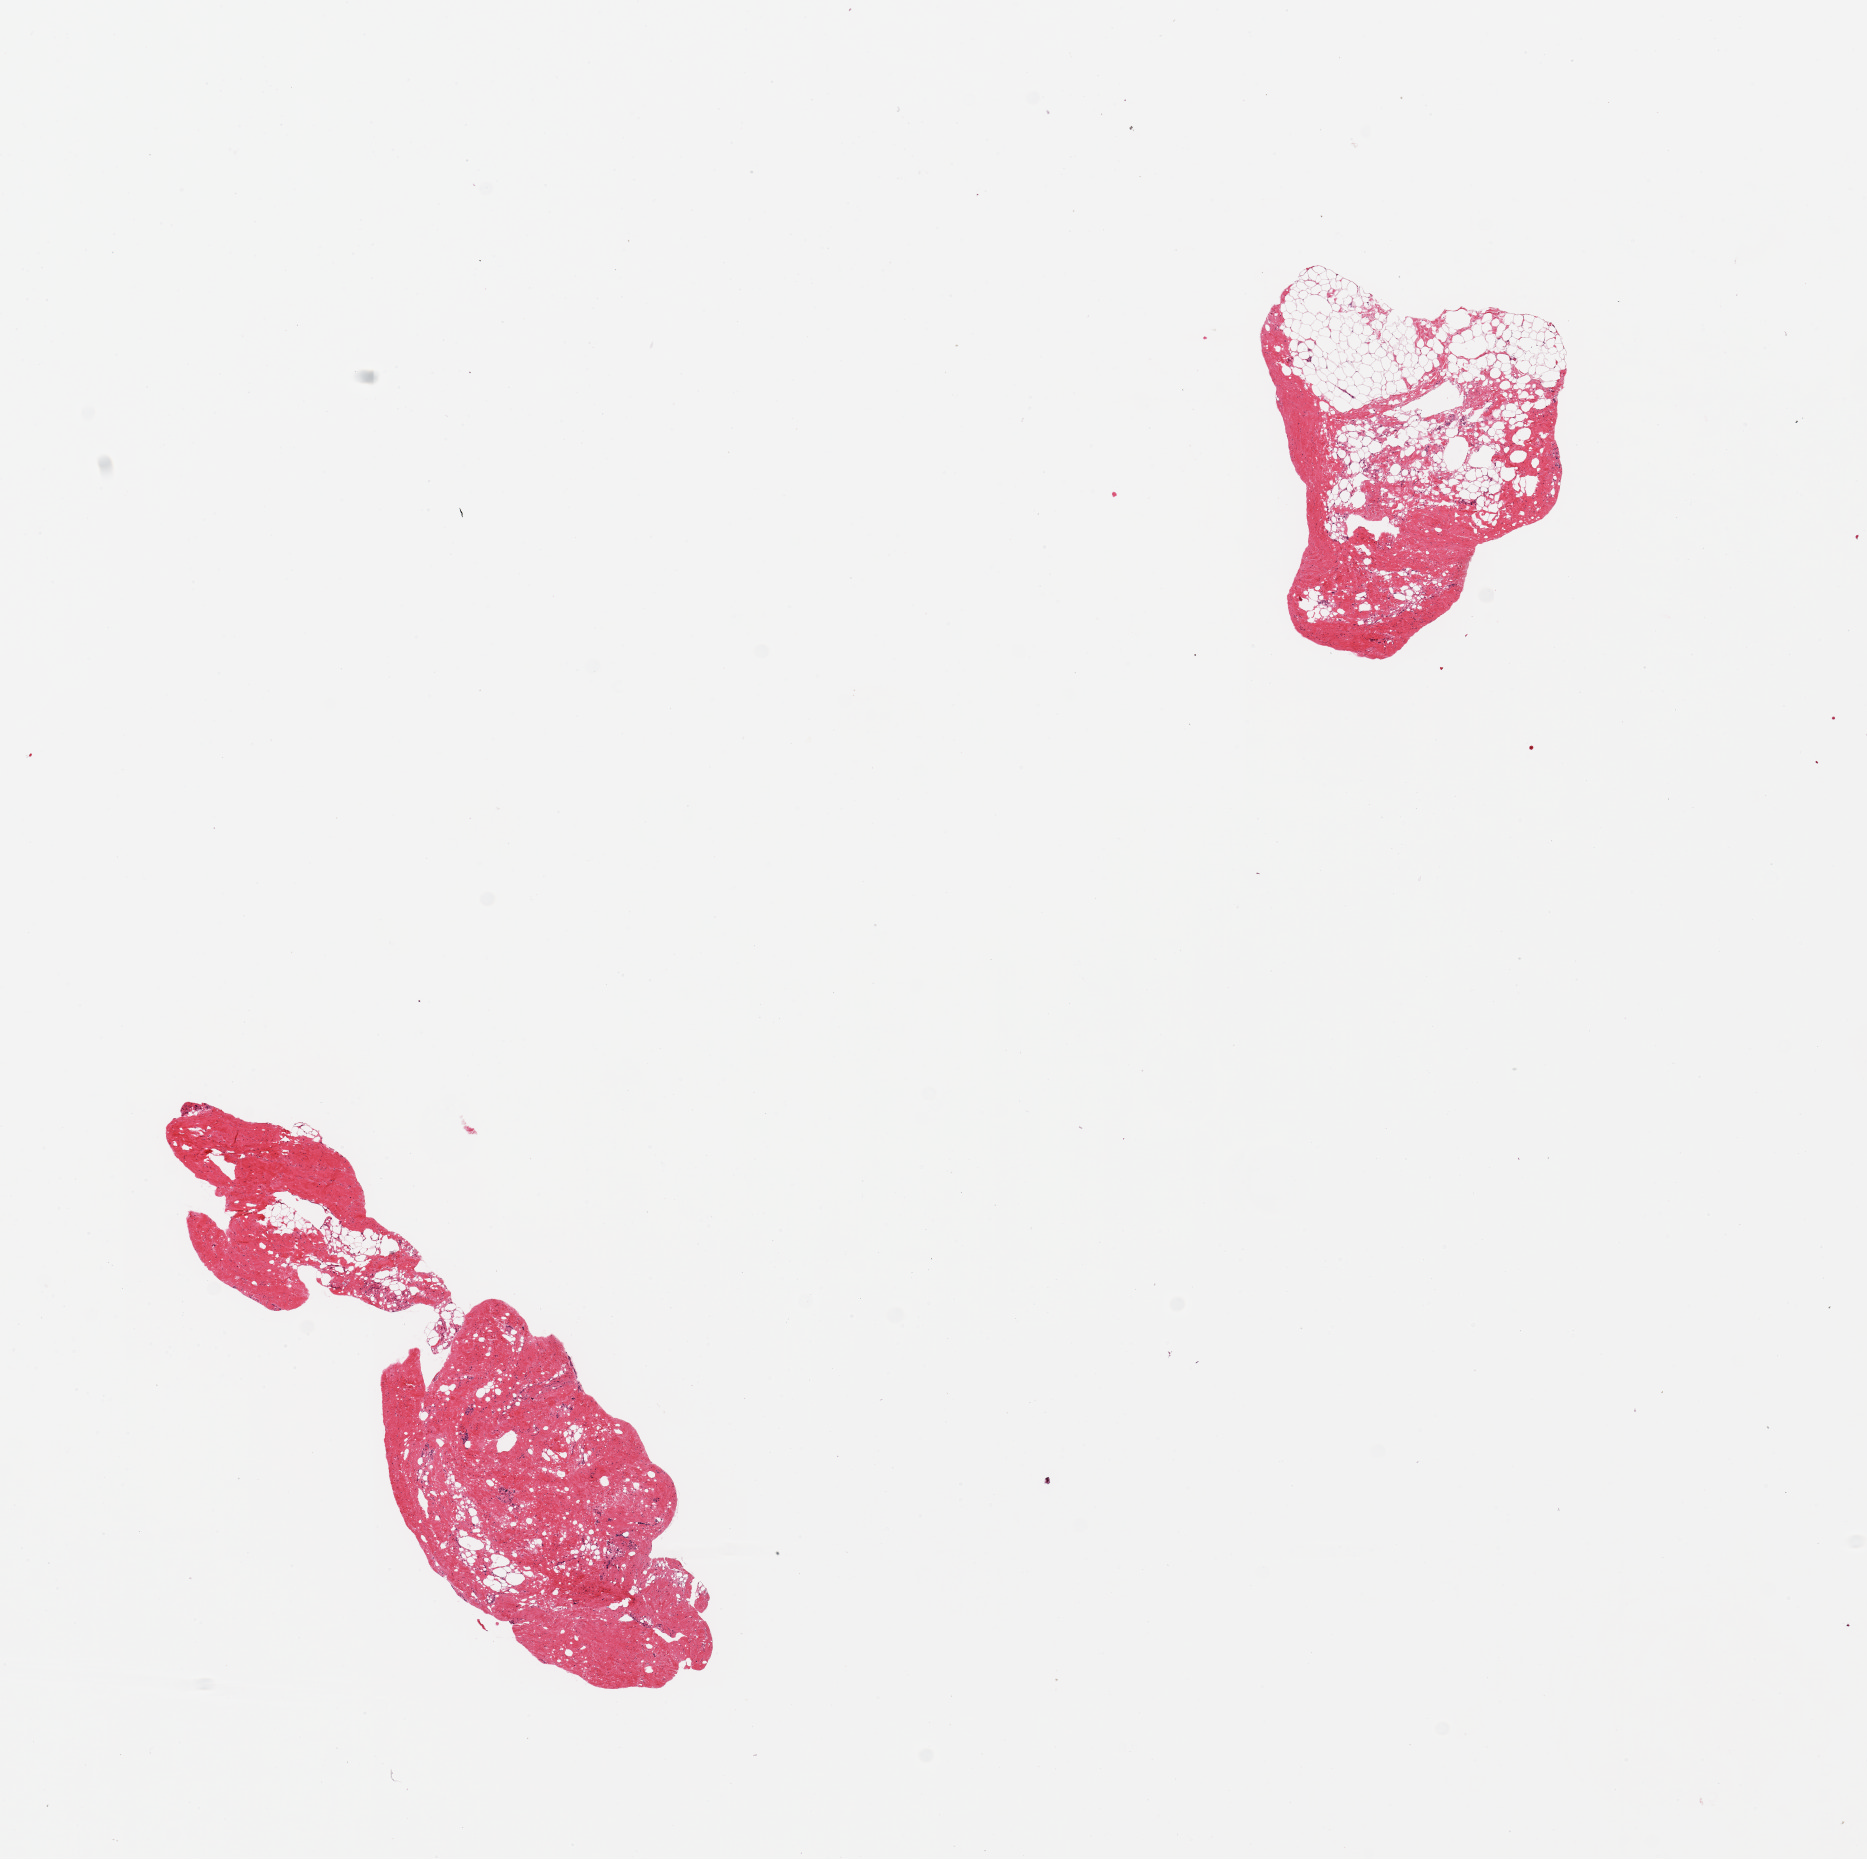
Digitized hematoxylin and eosin (H&E)-stained section — whole scanned area (about 14.8 x 14.7 mm) shown as a low-resolution overview. PAXgene-fixed, paraffin-embedded tissue. Sampled site (target tissue): breast. Tissue donor sample. Male donor.
Pathologist's review note for this sample: 2 pieces; fibroadipose tissue with no obvious ducts.